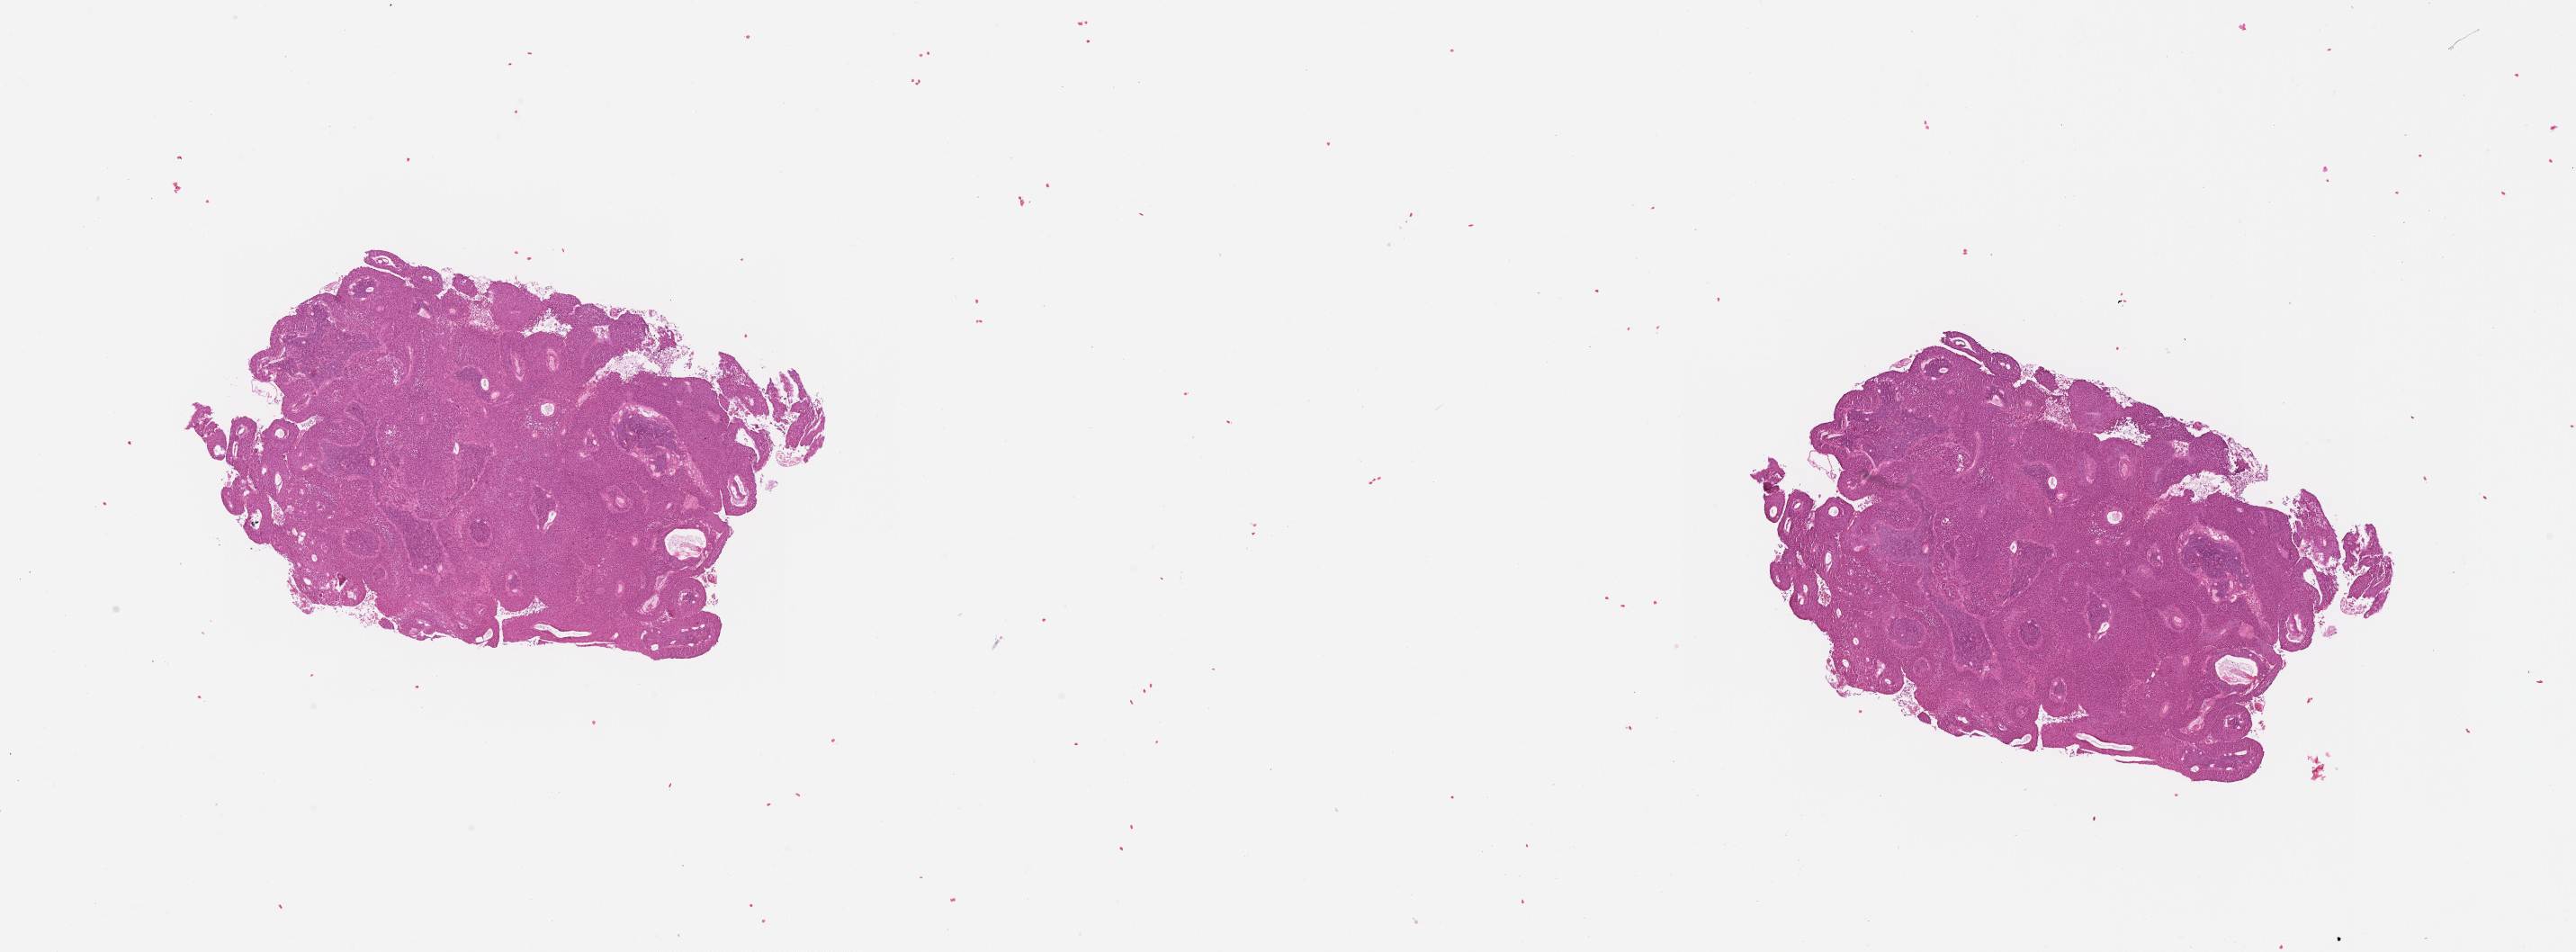
H&E whole-slide image — low-resolution overview of the scanned area, about 23.1 x 8.5 mm, lung, tissue type not recorded.
Patient diagnosis (cohort enrolment): squamous cell carcinoma (lung).